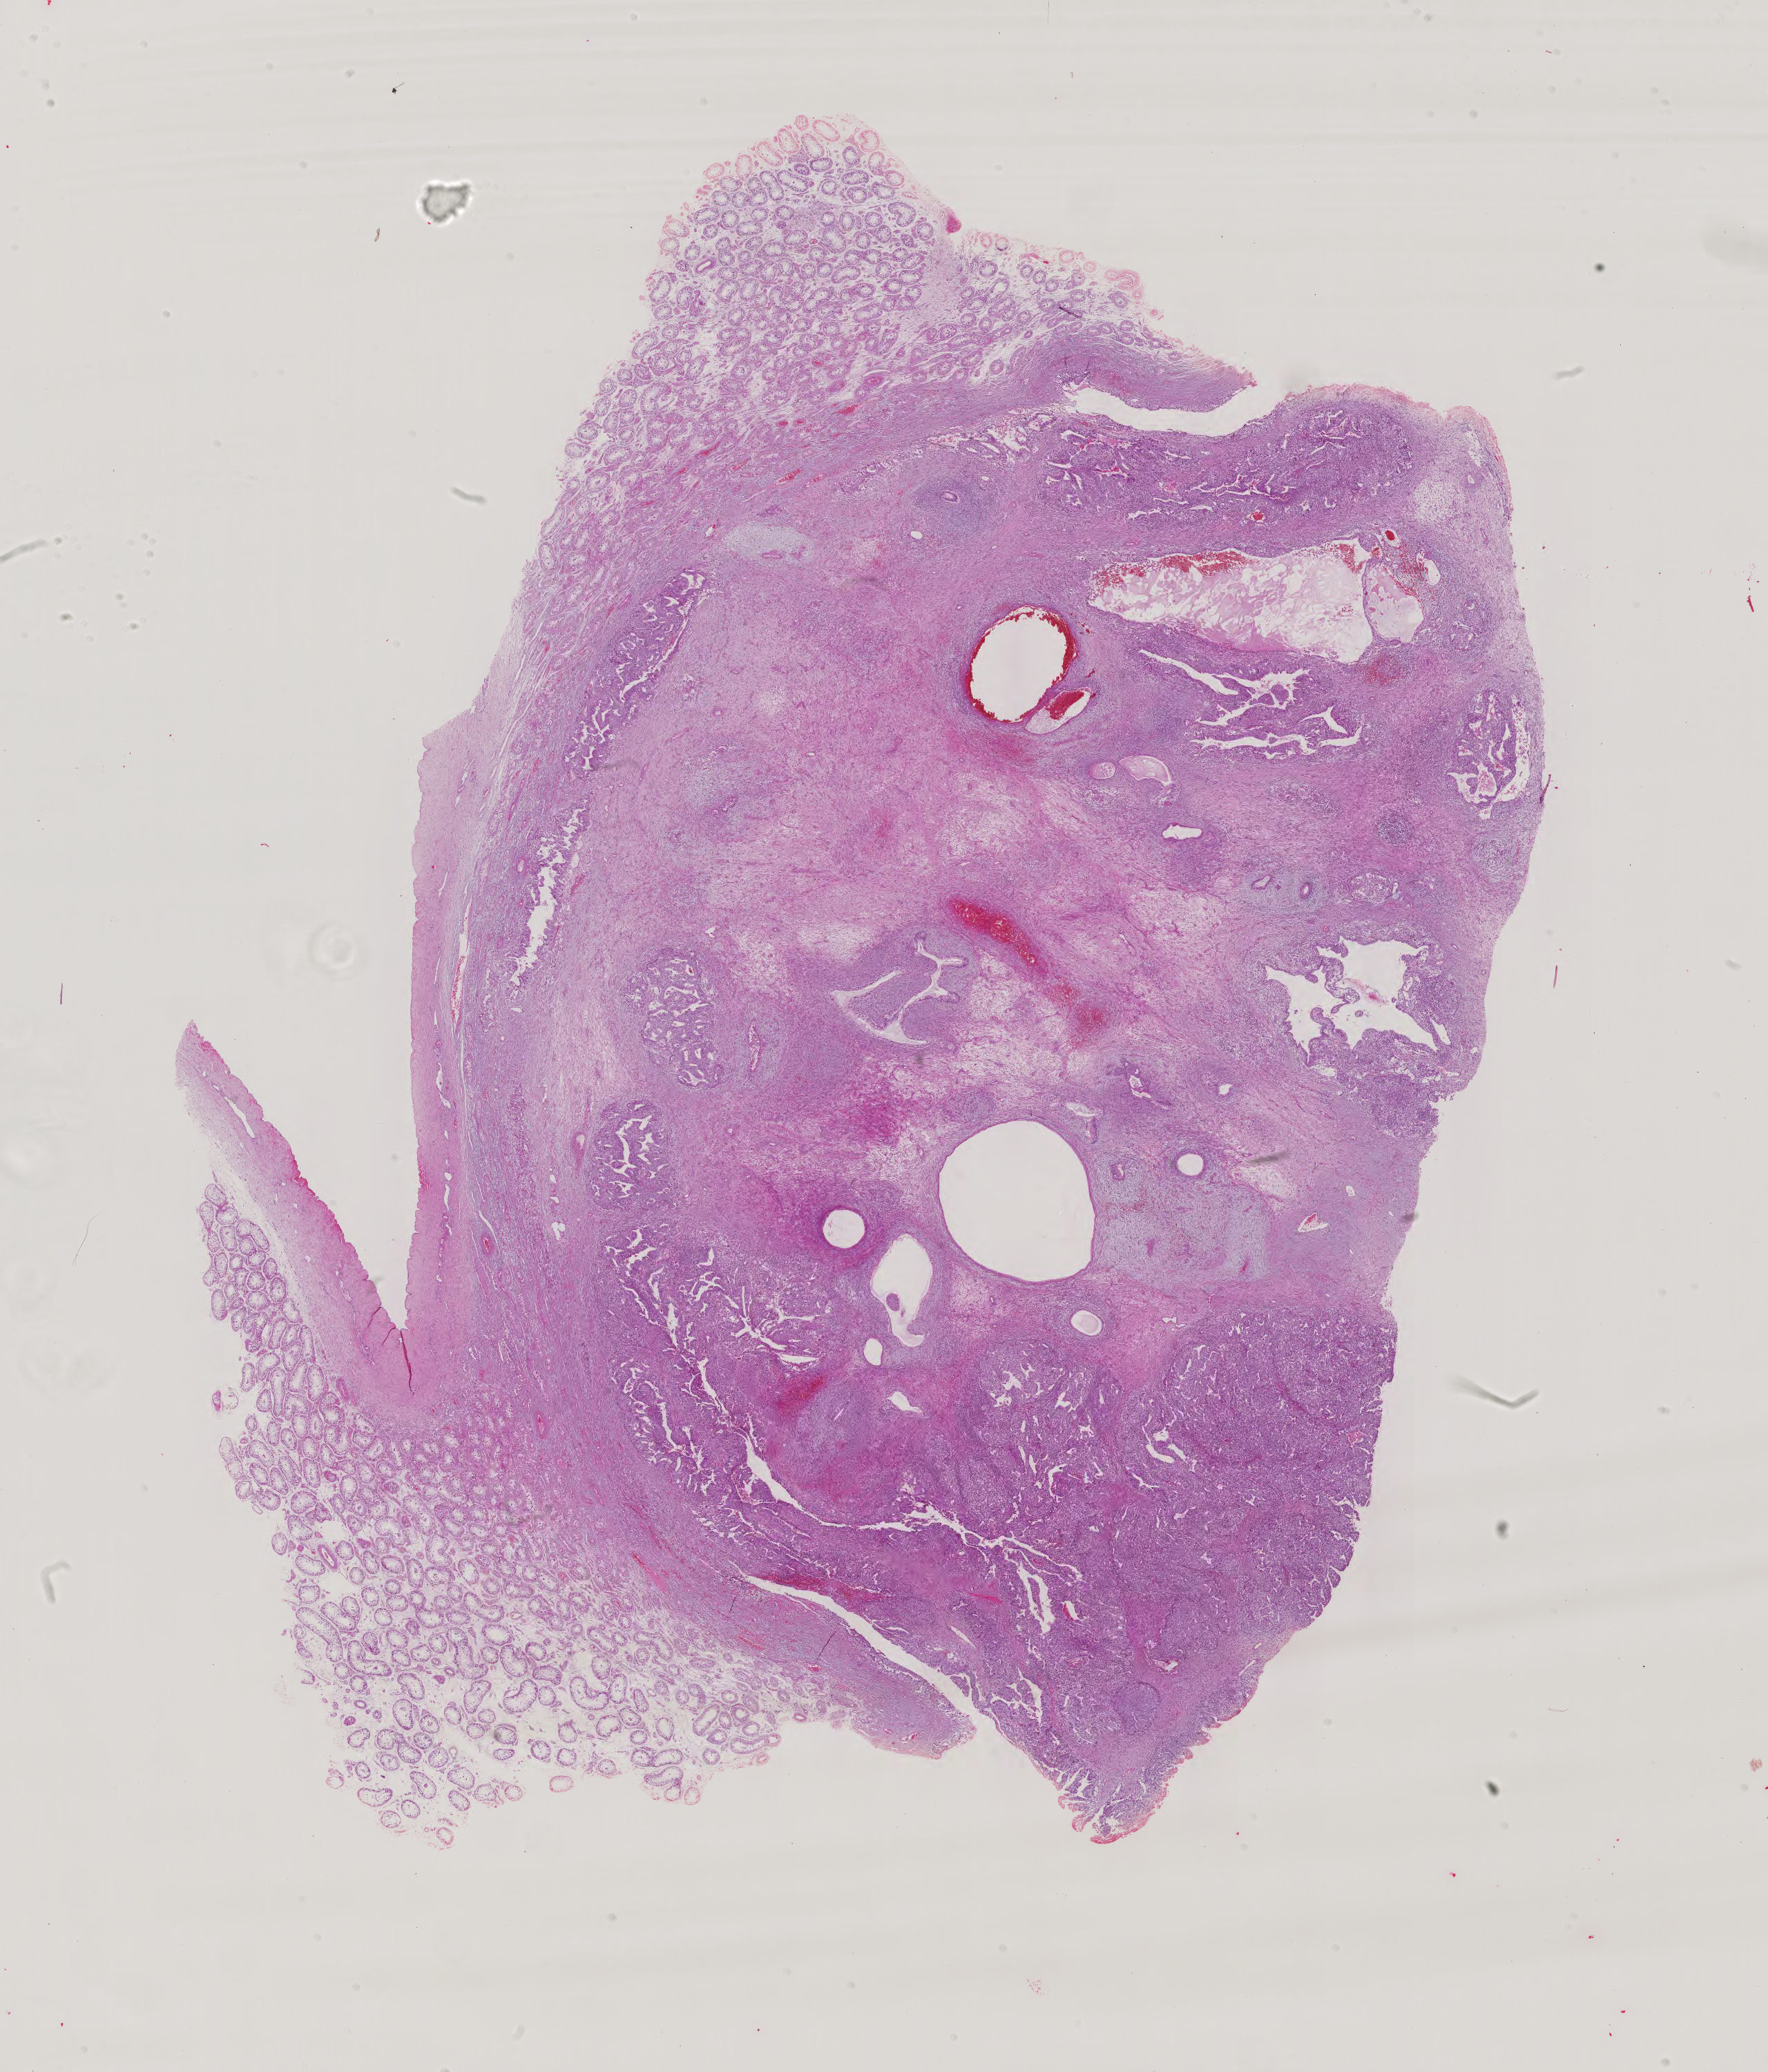
Whole-slide histology image, H&E, a low-resolution overview of the entire scanned area, about 18.7 x 21.9 mm (slide scanned at 40x). Patient sex: male.
Specimen: formalin-fixed paraffin-embedded (FFPE) diagnostic section; primary tumour sample from the testis.